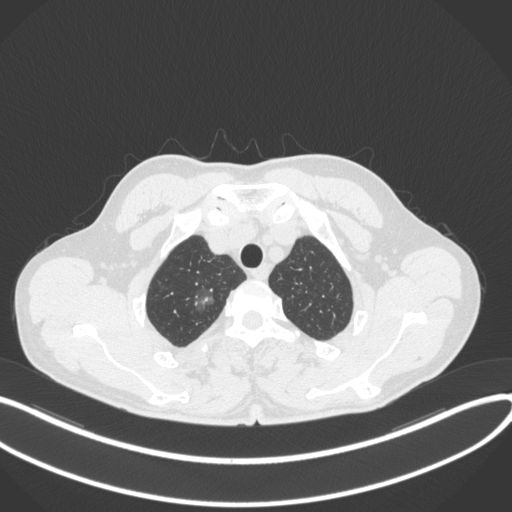
Chest CT, one axial slice. Position 332 of 407 along the scan axis. 120 kVp. Lung window (W 1500 / L -600 HU). 1 mm slice thickness. 512 × 512 image matrix, field of view 400 × 400 mm. Male patient, age 58 years. From the clinical record (not read from this slice): clinical TNM (as recorded): T1c N0 M0; histopathological grade: G1-2.
Annotated regions visible in this slice (bounding box drawn by a radiologist):
- lung tumour (recorded histology: adenocarcinoma): bounding box (x1, y1, x2, y2) in pixels: (191, 280, 221, 314)